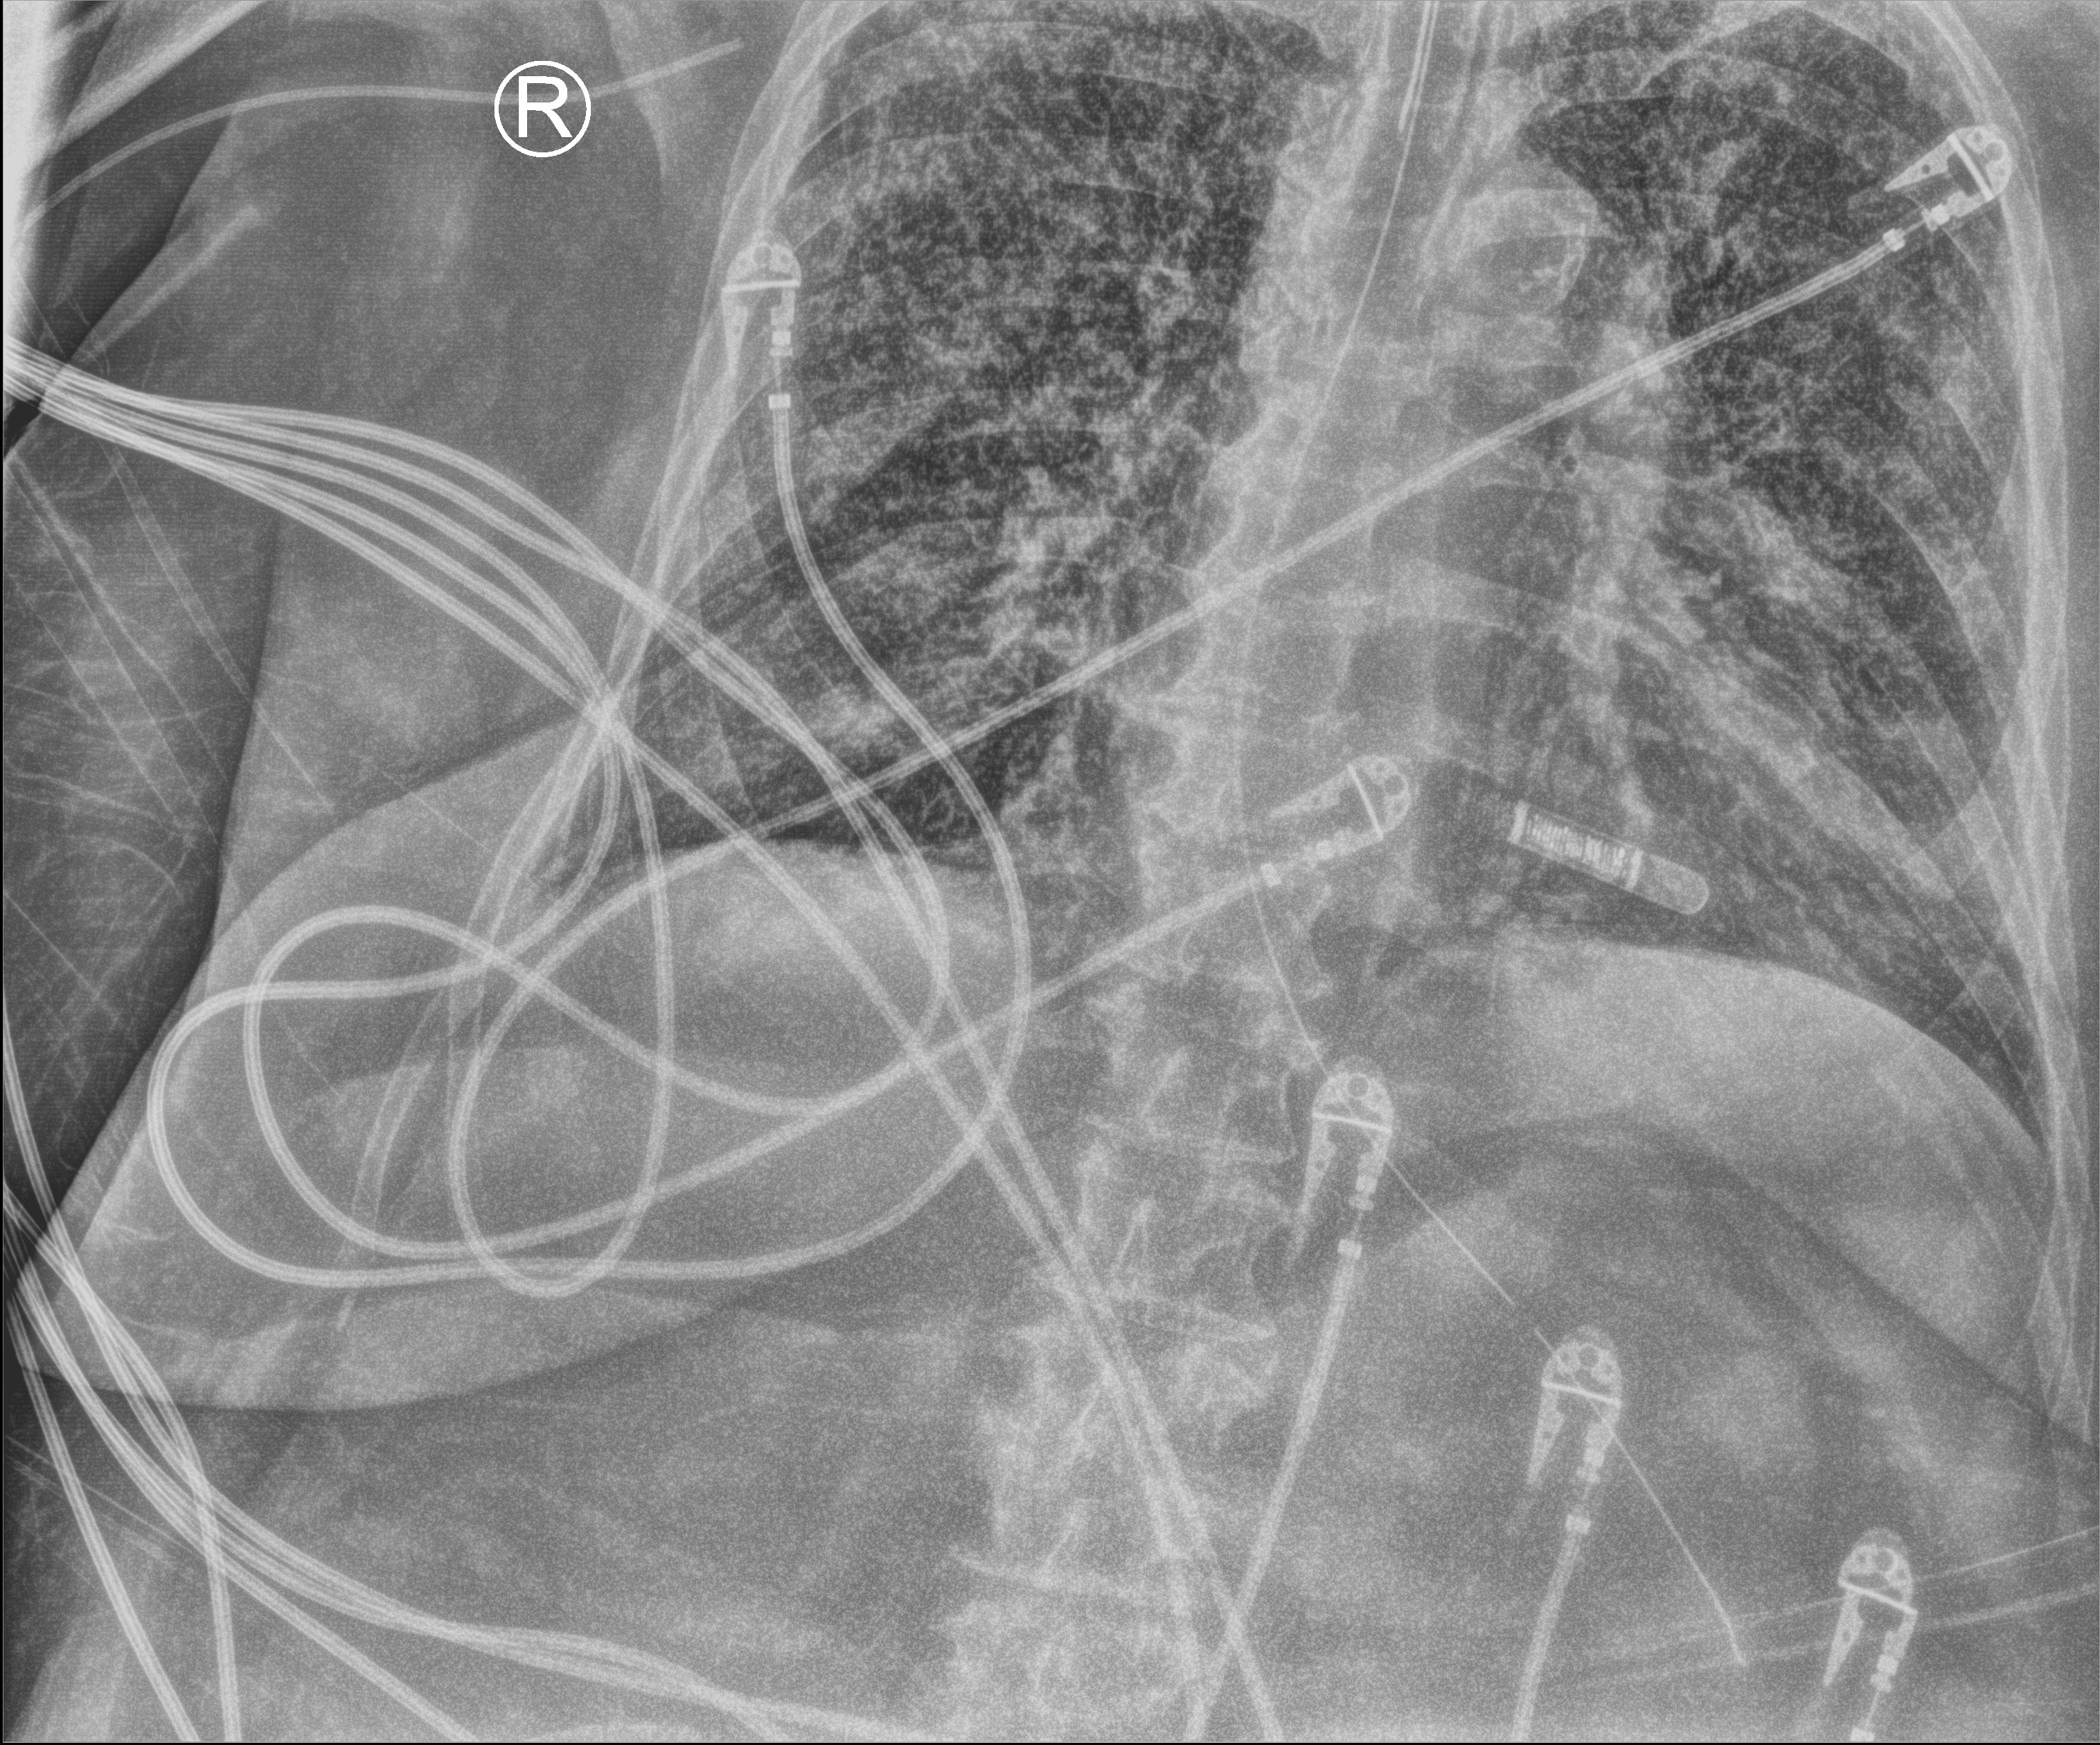
Portable chest radiograph. Female patient hospitalised with COVID-19, age 60–74 years.
Hospital-stay facts (about this admission, not read from this image; timing relative to this image not recorded): diabetes (admission record): yes.